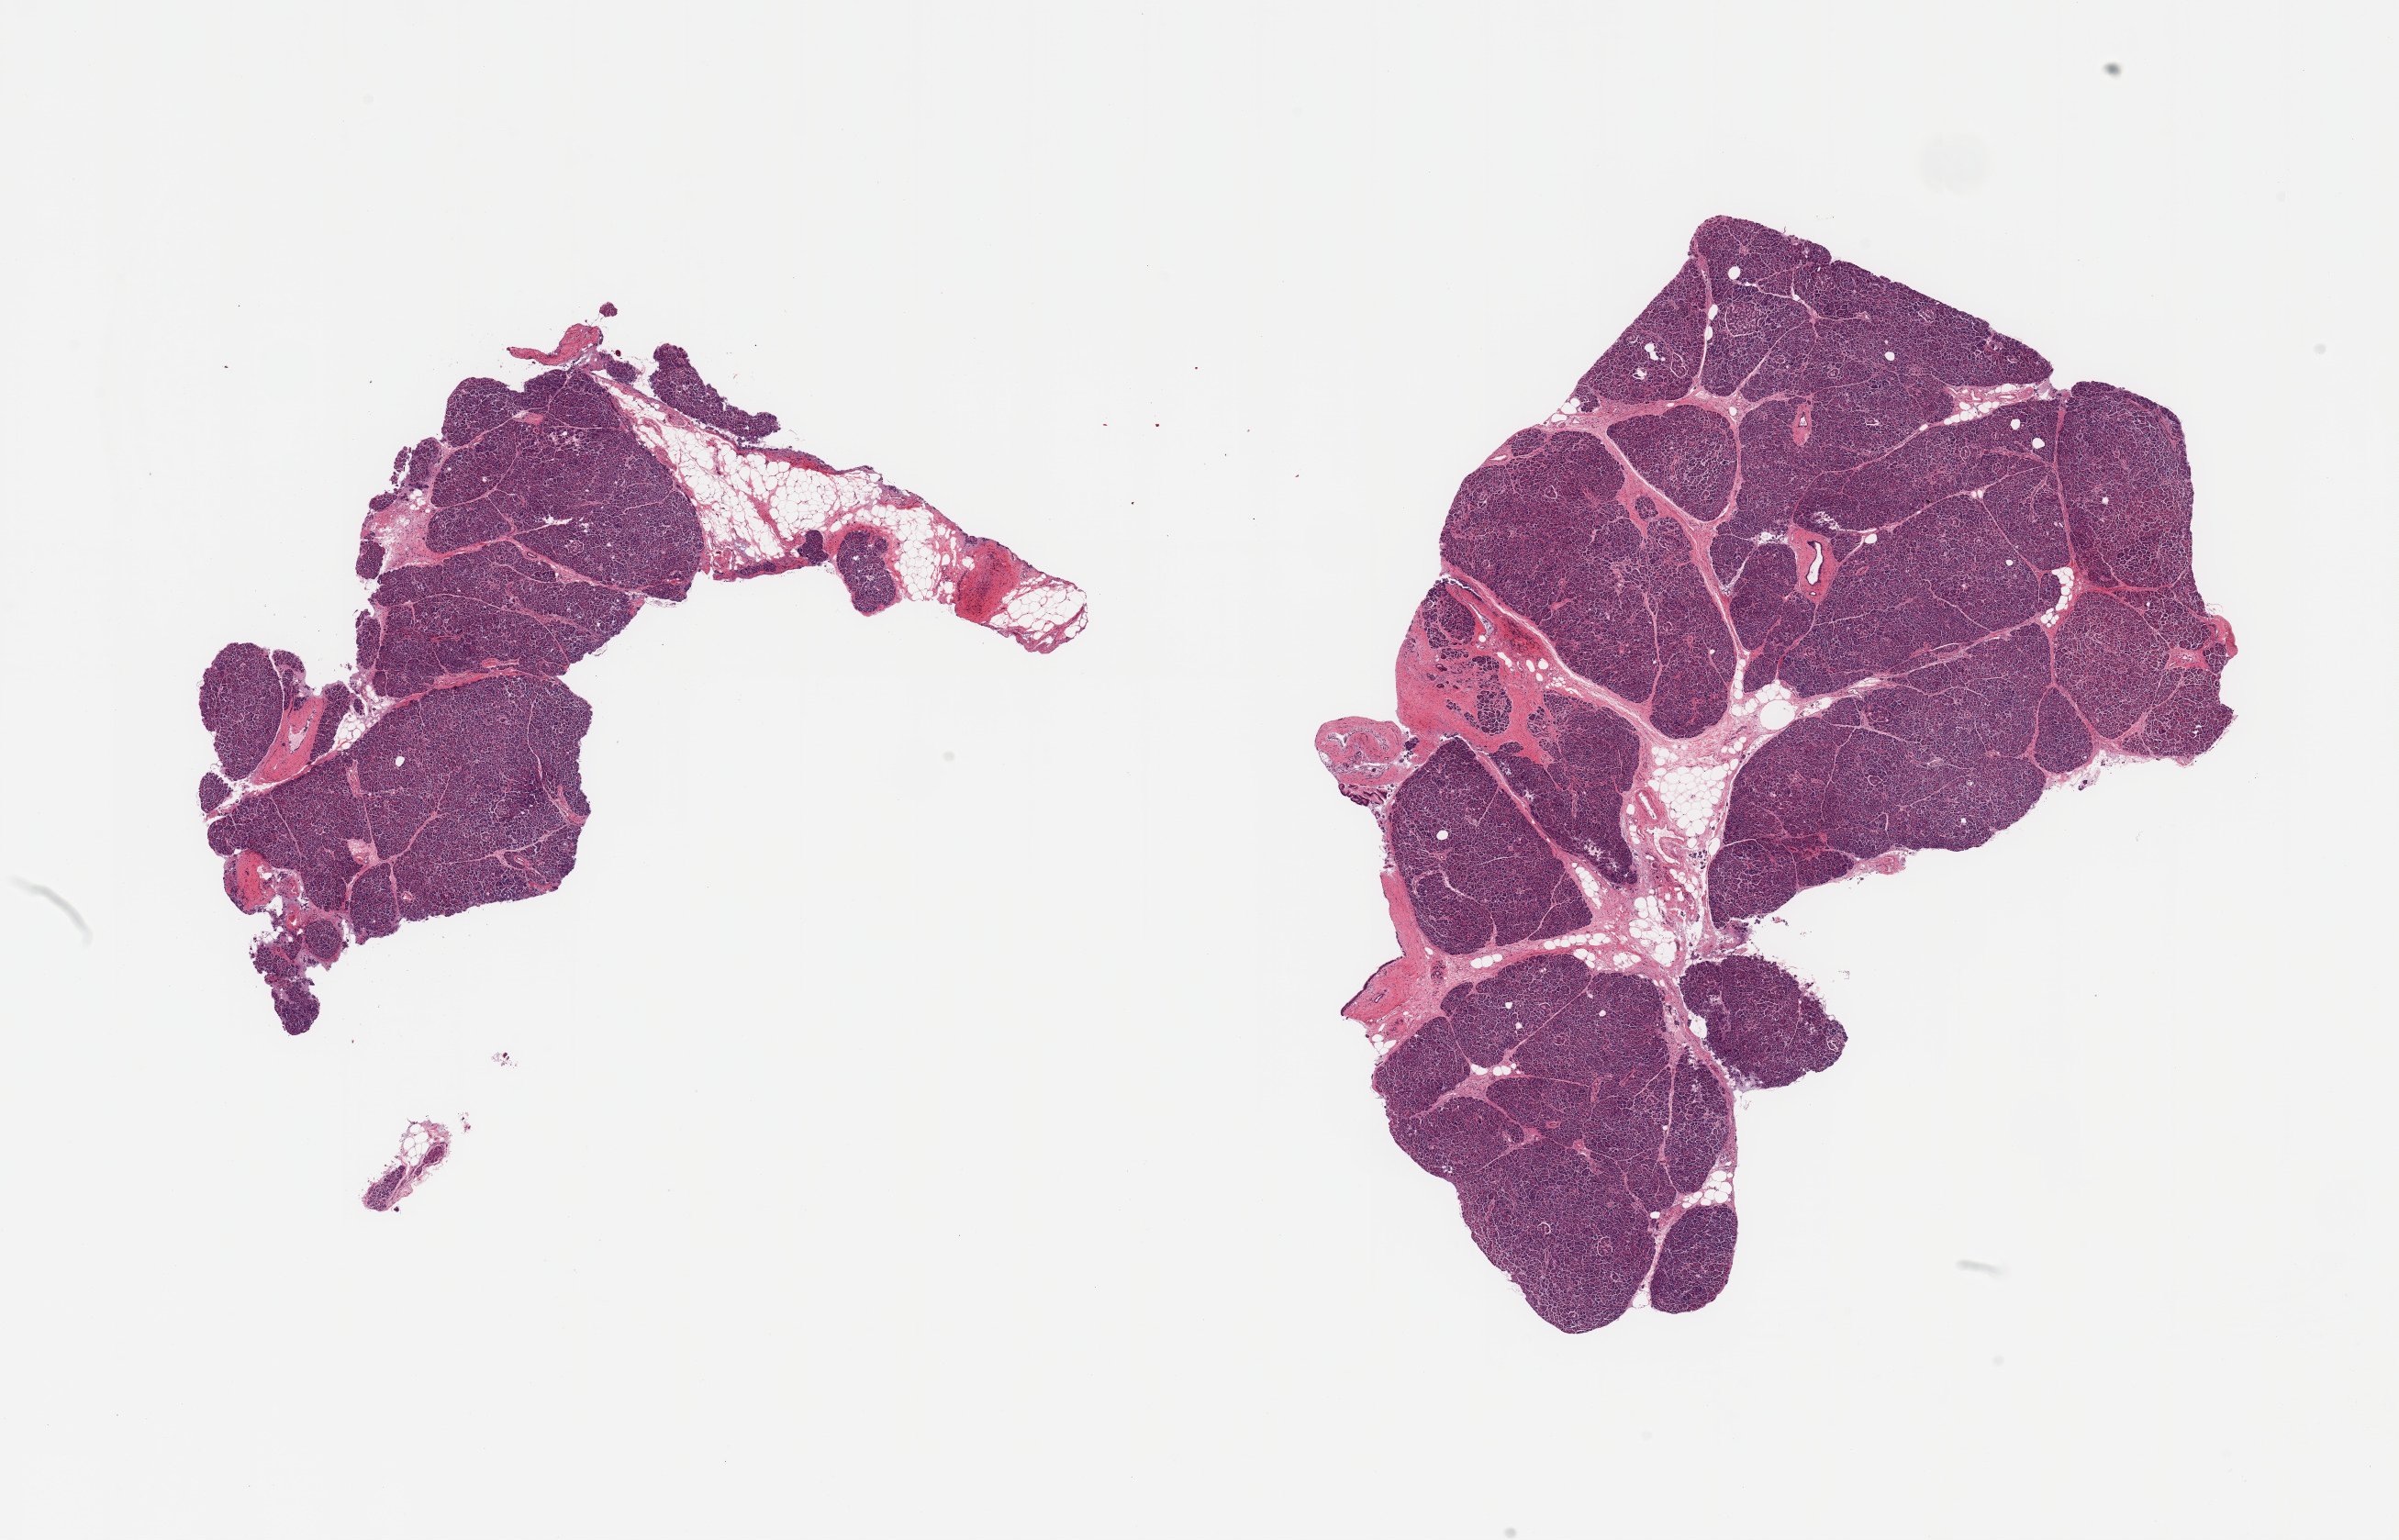
Digitized H&E-stained section, whole scanned area (about 20.7 x 13.3 mm, from a 20x scan) shown as a low-resolution overview, PAXgene-fixed, paraffin-embedded tissue, sampled site (target tissue): pancreas, tissue donor sample.
• review note (as recorded): 2 pieces, mild-moderate saponification; Islets rare, early degnerative changes